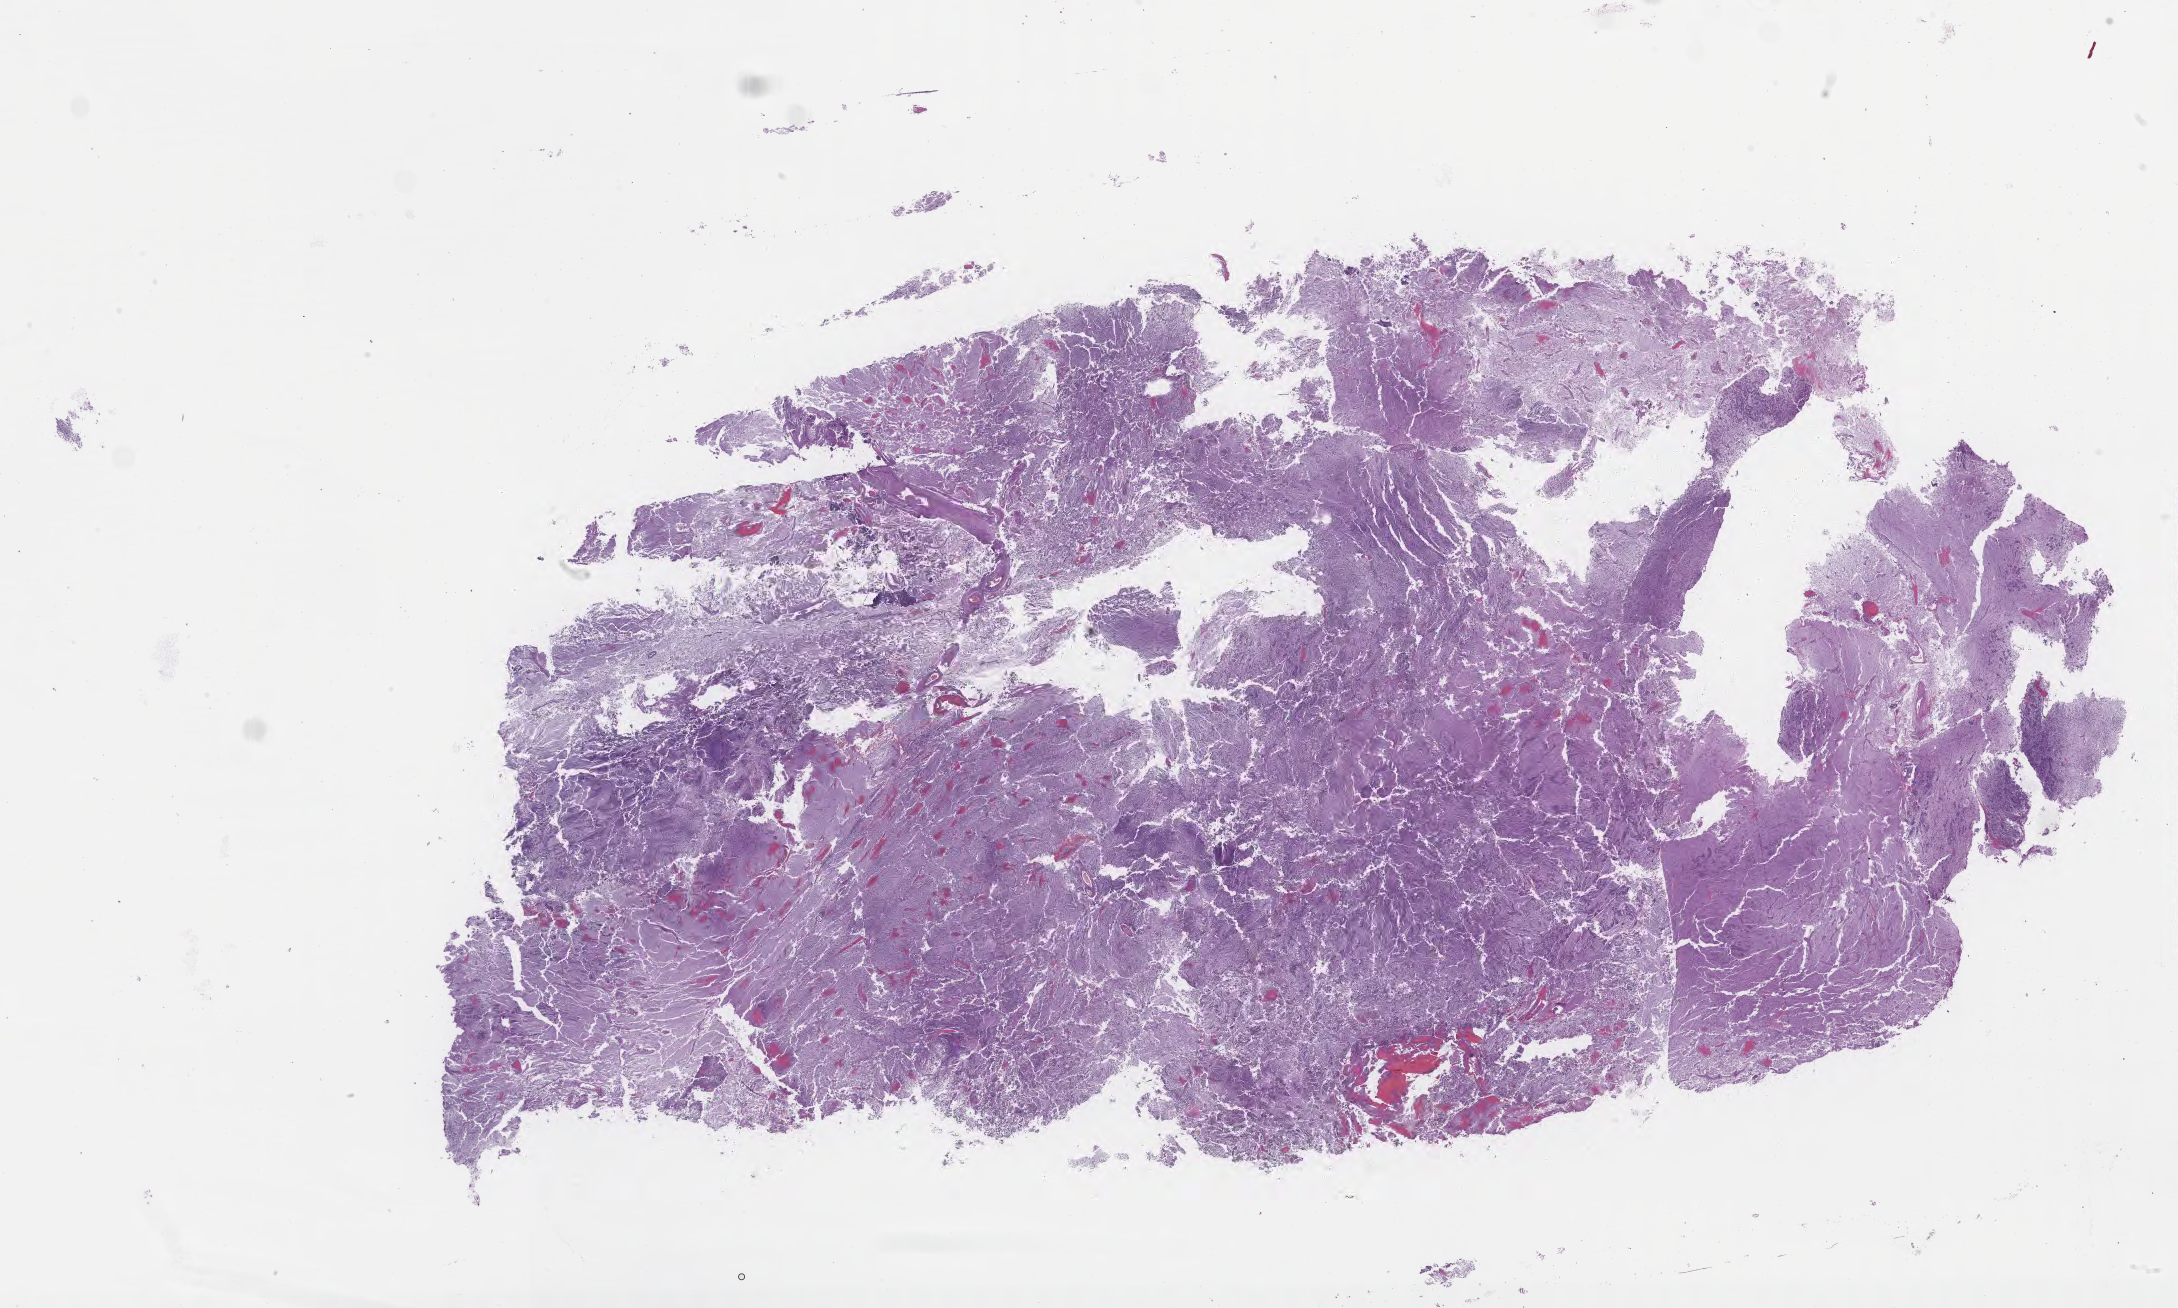
Digitized haematoxylin and eosin-stained section of tumor tissue from the brain — shown as a low-resolution overview of the whole scanned area (about 35.2 x 21.2 mm), formalin-fixed, paraffin-embedded (FFPE) tissue. Patient: female, age 39 months (3 years 3 months).
• diagnosis (ICD-O-3 morphology term): Embryonal carcinoma, NOS